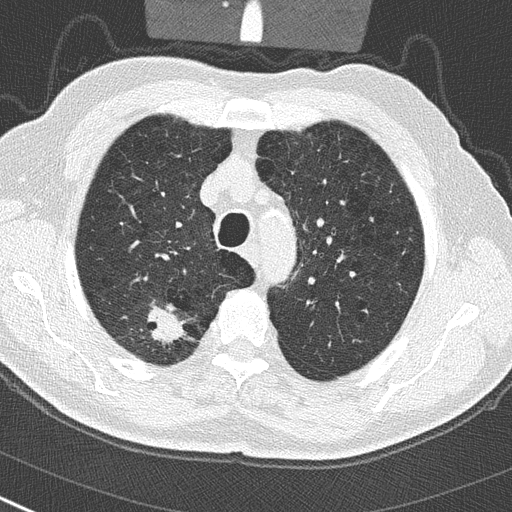
Axial slice from a low-dose chest CT screening exam, baseline screening round, lung window (W 1500 / L -600 HU), lung (sharp) reconstruction kernel (B50f), slice 66 of 290 in the series, 512 × 512 image matrix, field of view 300 × 300 mm. Male participant, aged 65 years at enrolment. Current smoker at enrolment.
Expert reader's lesion annotation, bounding box (x1, y1, x2, y2) in pixels: (131, 300, 195, 358). Screening reader's record for this exam (one nodule recorded; not confirmed to be the boxed lesion): non-calcified nodule or mass ≥4 mm, right upper lobe, 24 × 19 mm, spiculated (stellate) margins, soft tissue attenuation. Lung cancer was diagnosed 32 days after this screen: non-small cell carcinoma, right upper lobe, poorly differentiated (G3), stage IA (AJCC 6th edition), 29 mm at pathology.